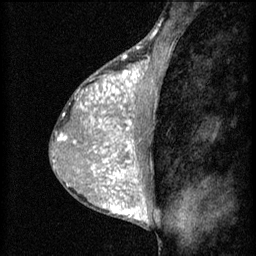
Breast MRI (dynamic contrast-enhanced), one sagittal slice; slice 32 of 60 in the series (ordered by position); 3 images stored at this slice position (order not interpretable as contrast timing); 1.5 T; TE 4.2 ms, TR 8.2 ms; 2 mm slice thickness; 256 × 256 image matrix. Patient: female, 38 years.
Annotated regions visible in this slice (semi-automatically segmented with operator editing):
- analysis volume of interest (the breast-tissue region the enhancement analysis was run in; not a lesion): bounding box (x1, y1, x2, y2) in pixels: (95, 106, 155, 171)
- tumour enhancement mask (voxels above the 70 % enhancement threshold inside the analysis volume of interest): (95, 106, 140, 171)